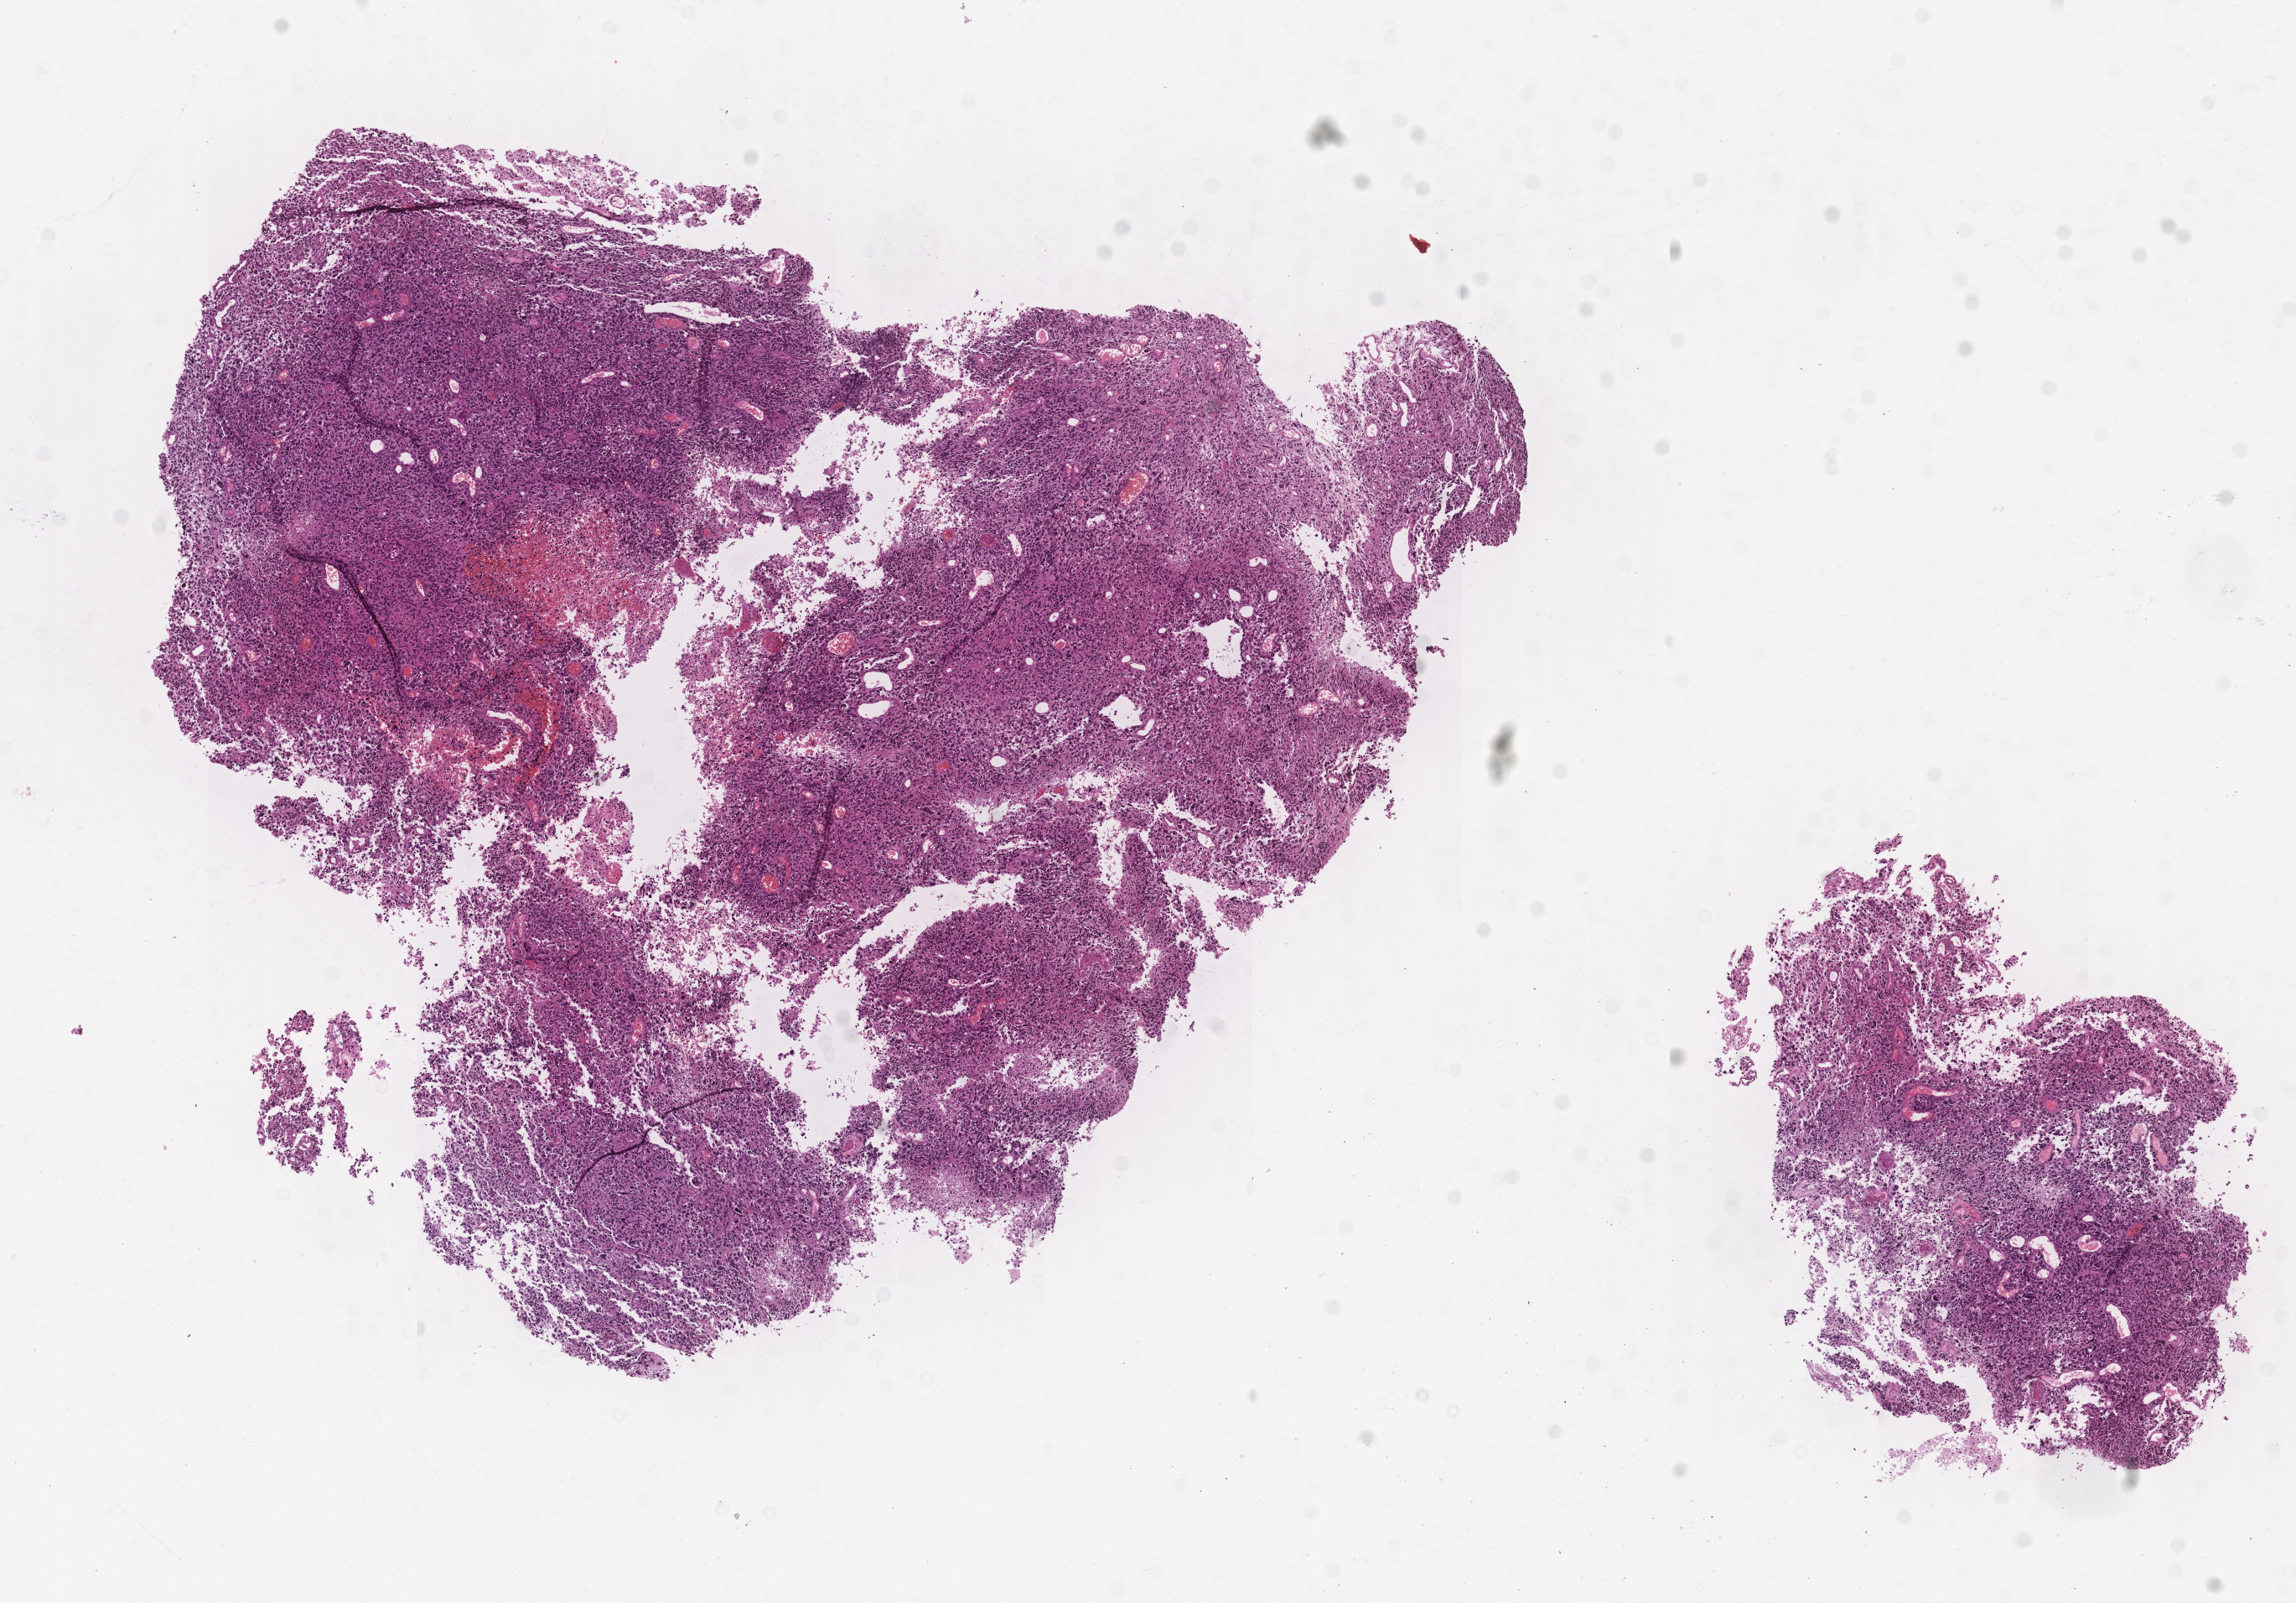
Digitized H&E-stained tissue section (whole slide) — shown as a low-resolution overview of the whole scanned area (about 11.0 x 7.7 mm, from a 20x scan). Tumour tissue sample, brain. 65-year-old male patient.
* histologic diagnosis: Glioblastoma
* primary tumour site (as recorded): temporal lobe